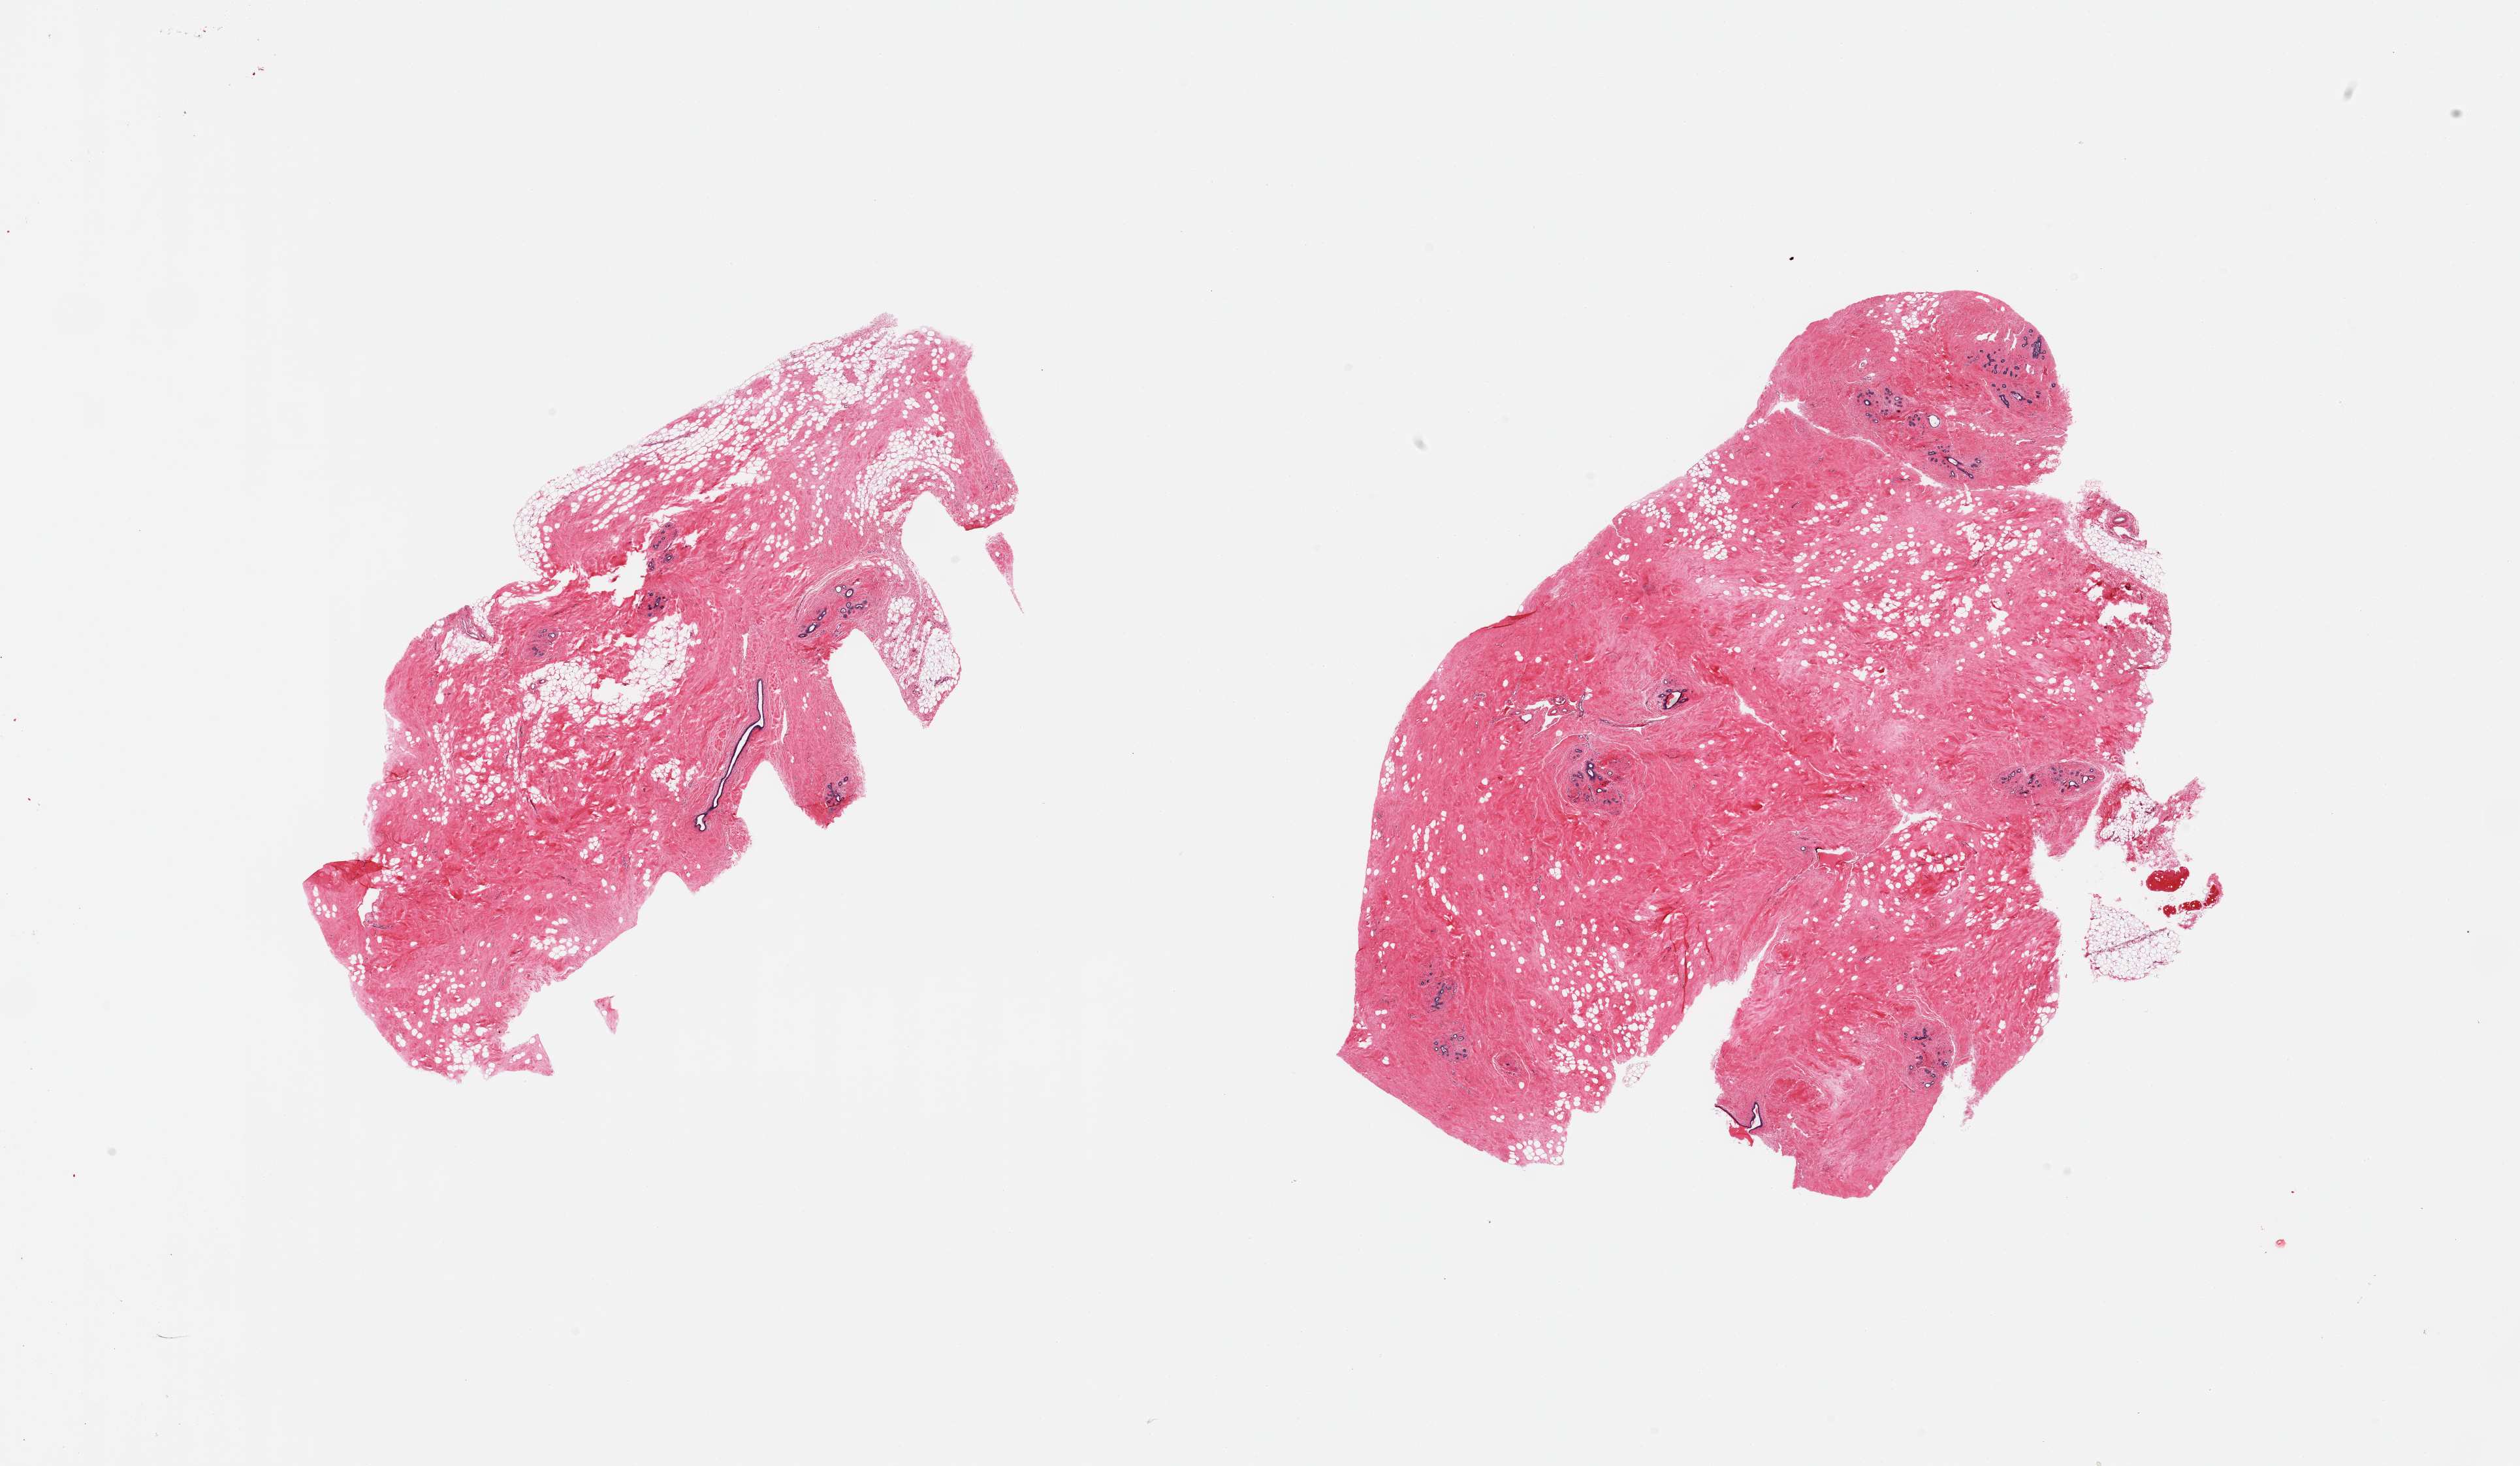
Digitized H&E-stained section — a low-resolution overview of the entire scanned area, about 30.5 x 17.8 mm (from a 20x scan). PAXgene-fixed, paraffin-embedded tissue. Section of breast (target tissue). Tissue donor sample. Donor sex: female.
• pathologist's review note for this sample: 2 pieces, fibrous mastopathy; Rare atrophic duct/lobular units